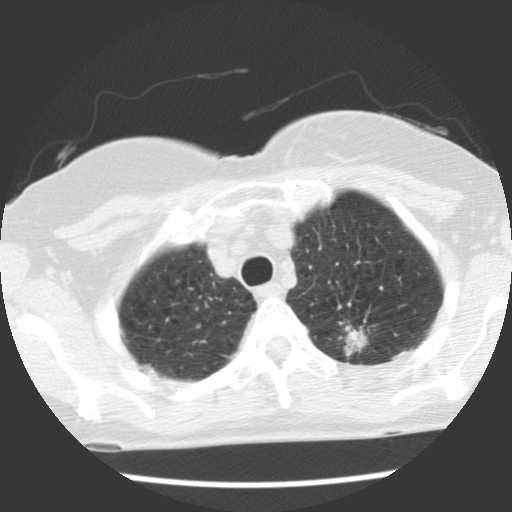
Low-dose screening chest CT, one axial slice; position 97 of 120 along the scan axis; reconstruction kernel STANDARD; 140 kVp; lung window (W 1500 / L -600 HU); 512 × 512 image matrix.
Structures marked on this image (manually delineated by an expert):
- lesion 1 (tumor, upper lobe of left lung): box from (x=344, y=325) to (x=367, y=356) px